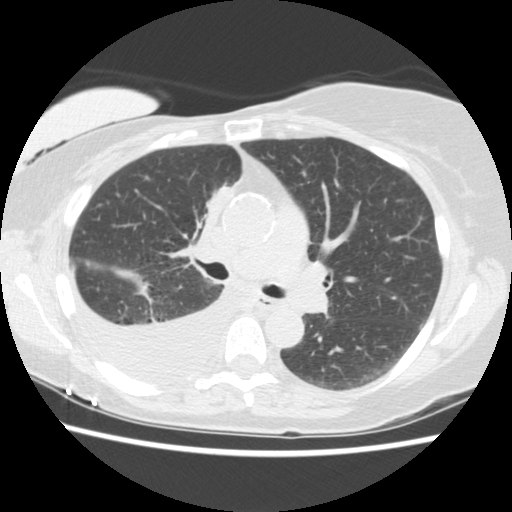
Low-dose screening chest CT, one axial slice; position 91 of 157 along the scan axis; reconstruction kernel STANDARD; 120 kVp; lung window (W 1500 / L -600 HU); 2.5 mm slice thickness; 512 × 512 image matrix.
Structures marked on this image (manually delineated by an expert):
- lesion 1 (tumor, upper lobe of right lung): bounding box (x1, y1, x2, y2) in pixels: (204, 184, 233, 226)